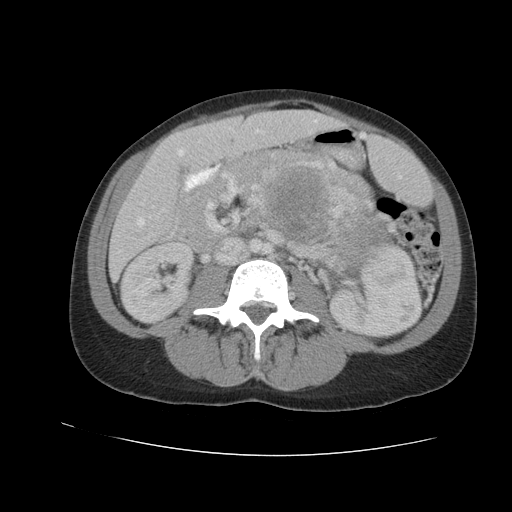
Contrast-enhanced abdominal CT, one axial slice; slice 51 of 90 in the series (ordered by position); 120 kVp; intravenous contrast given; soft-tissue window (W 400 / L 40 HU); 512 × 512 image matrix, field of view 360 × 360 mm. Female patient. Case-level facts recorded for this patient, not image findings: diagnosis: adrenocortical carcinoma; tumour side: left adrenal; tumour size at pathology: 18 cm; Ki-67 index: 11 %; stage (as recorded): 3.
Structures marked on this image (semi-automatic segmentation, software-assisted and operator-edited):
- mass: bounding box [x1, y1, x2, y2] px = [266, 167, 392, 268]